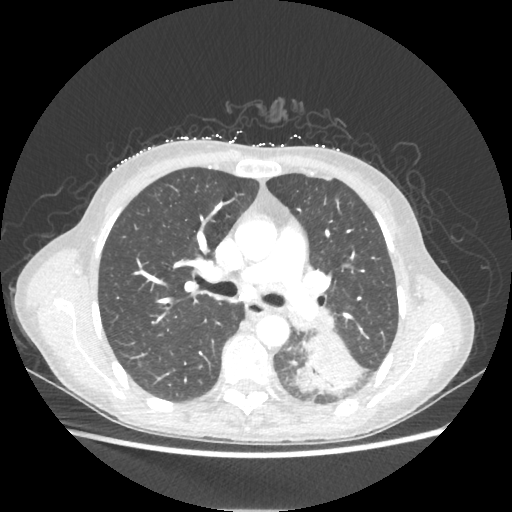
Chest CT, one axial slice; slice 134 of 221 in the series (ordered by position); 80 kVp; lung window (W 1500 / L -600 HU); 512 × 512 image matrix. Patient: female, 53 years. Case-level facts recorded for this patient, not image findings: clinical TNM (as recorded): T3 N0 M0.
Outlined on this slice (rectangle marked by the reading radiologist):
- lung tumour (recorded histology: adenocarcinoma): bounding box (x1, y1, x2, y2) in pixels: (293, 332, 361, 393)